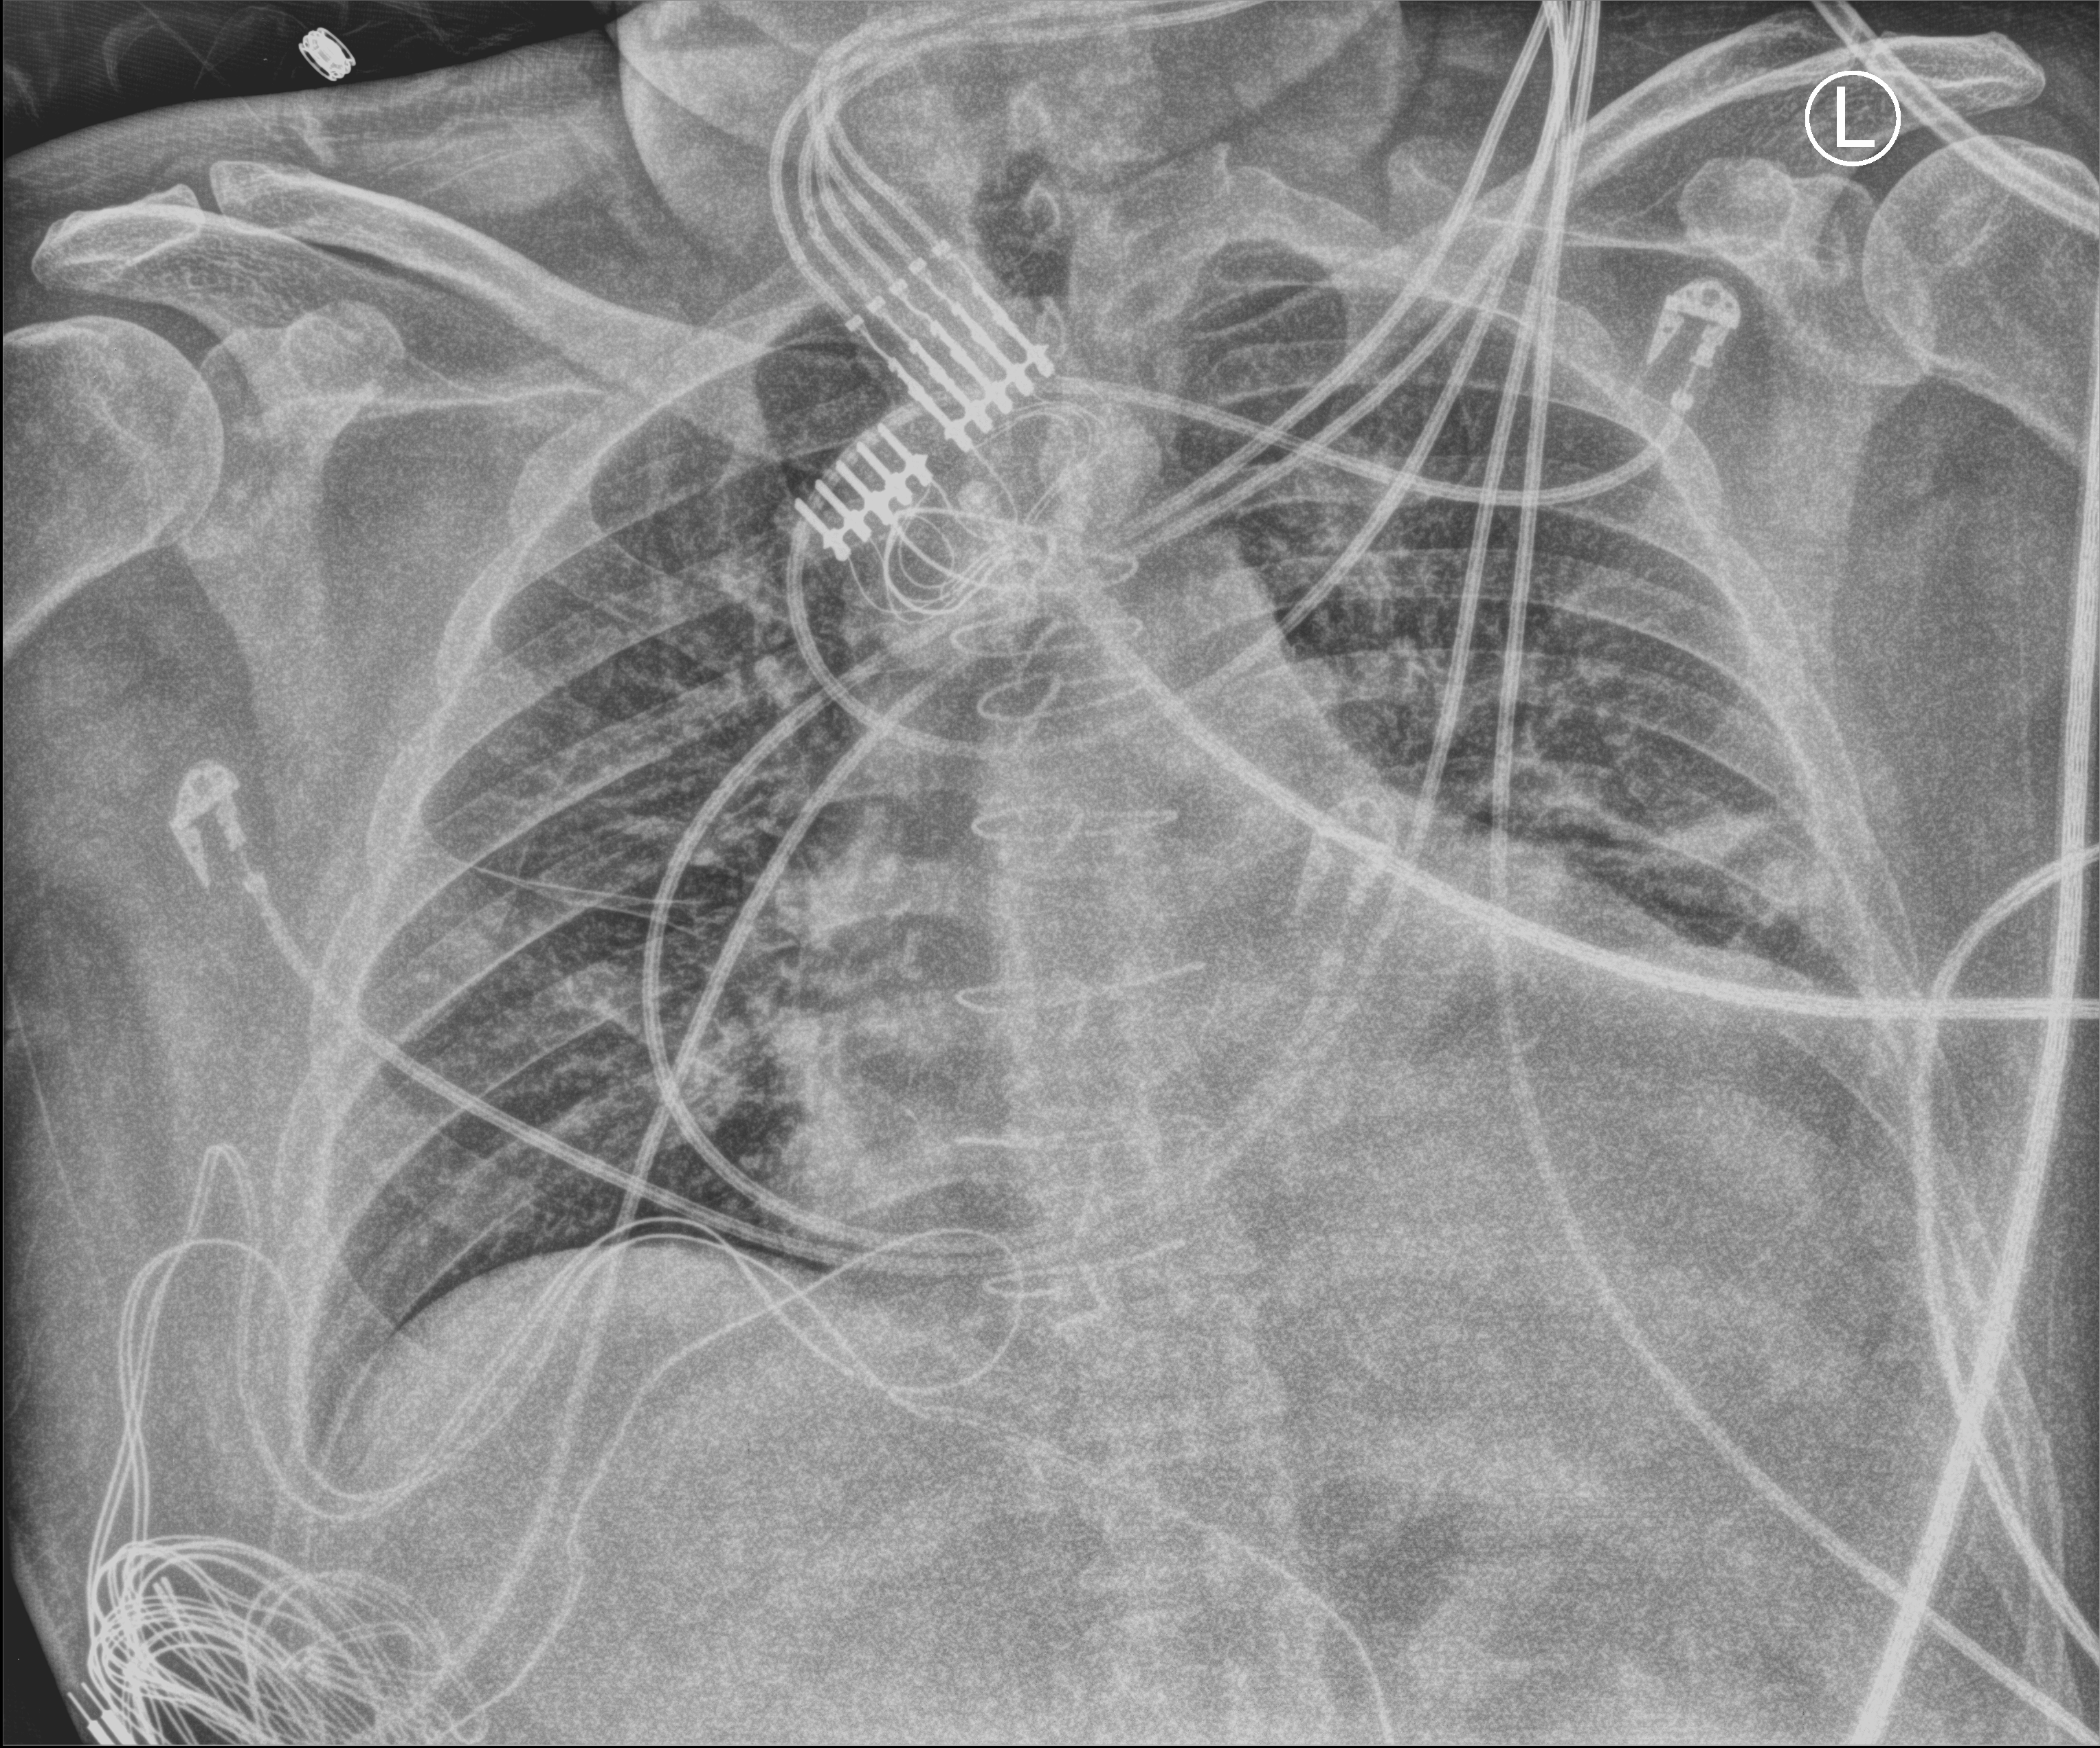
Bedside chest radiograph (computed radiography); anteroposterior (AP) projection. Patient hospitalised with COVID-19; male, aged 18–59 years.
Admission-level facts for this patient (not findings on this image; timing relative to this image not recorded):
- length of hospital stay: 17 days